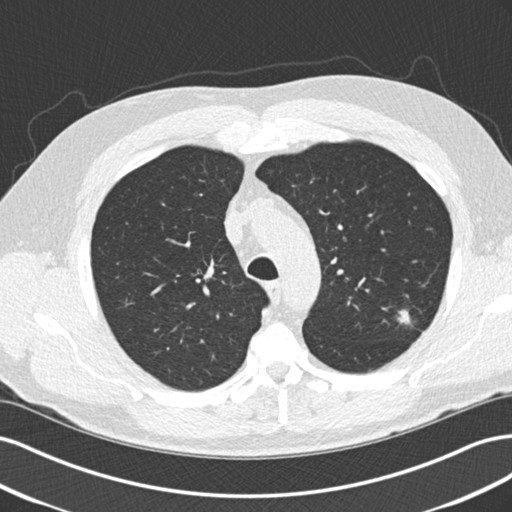
Low-dose screening chest CT, axial slice. Second screening round (one year after baseline). Lung window (W 1500 / L -600 HU). 2 mm slice thickness. Slice 50 of 209 in the series. 512 × 512 image matrix. Male participant, aged 65 years at enrolment.
Expert-annotated lung lesion, bounding box (x1, y1, x2, y2) in pixels: (387, 304, 425, 341). Screening reader's record for this exam (one nodule recorded; not confirmed to be the boxed lesion): non-calcified nodule or mass ≥4 mm, left upper lobe, 10 × 9 mm, poorly defined margins, mixed attenuation, pre-existing on the prior screen: yes; interval growth: no. Participant outcome: lung cancer diagnosed 221 days after this screen — adenocarcinoma, NOS, left upper lobe, poorly differentiated (G3), stage IA (AJCC 6th edition), 13 mm at pathology.